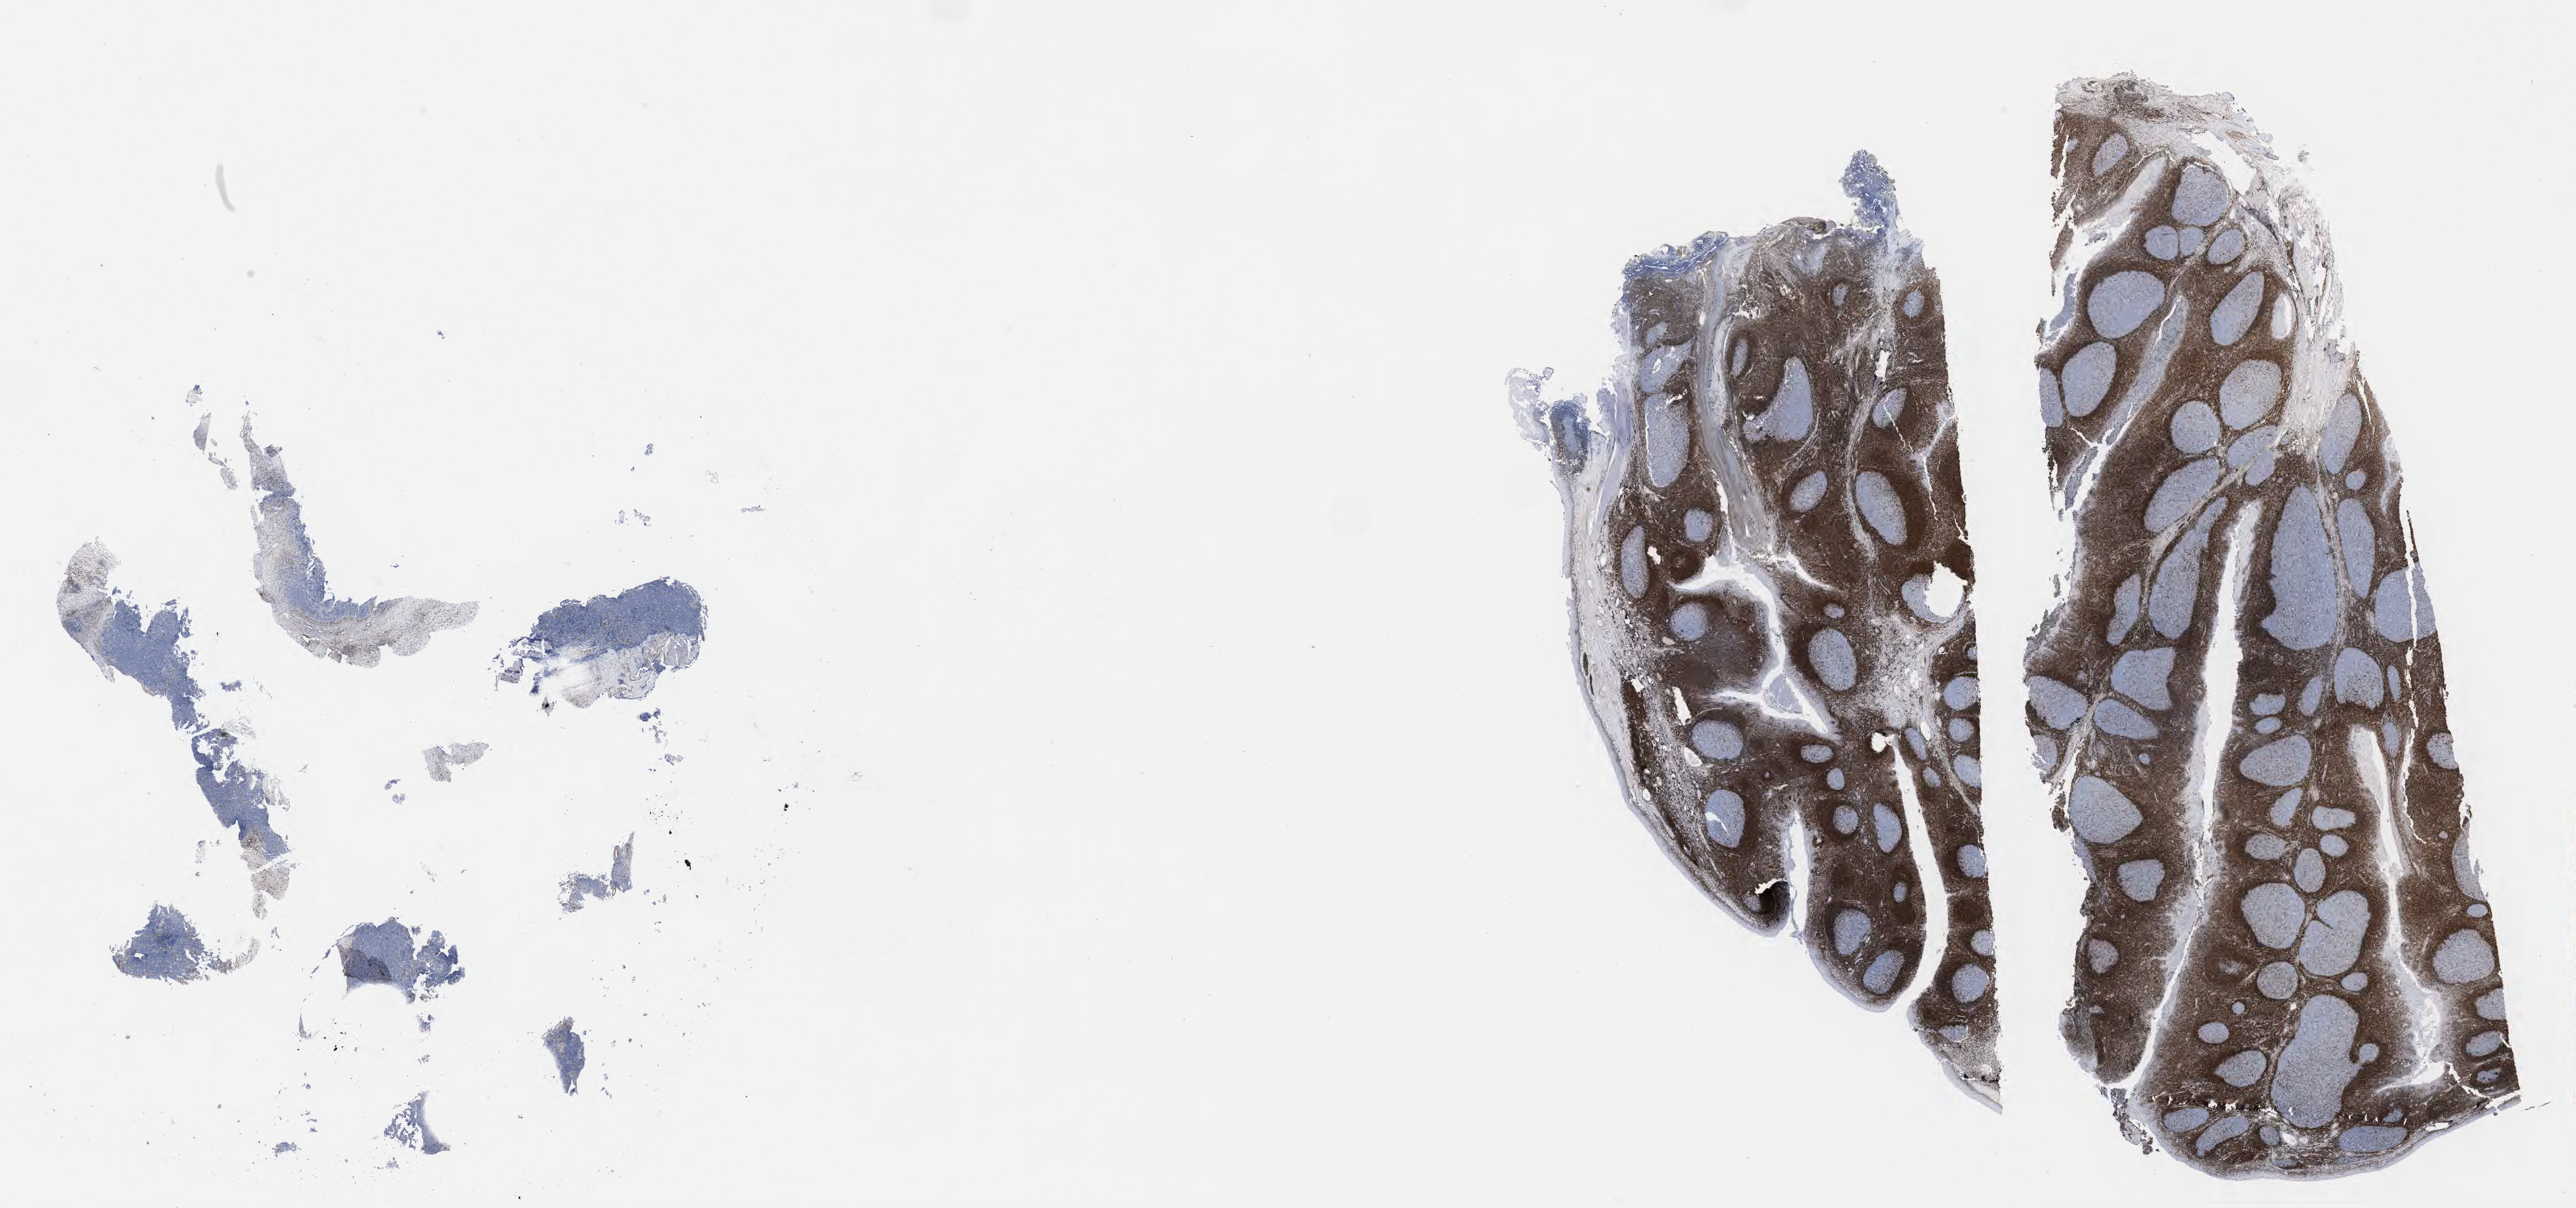
IHC for BCL2, whole-slide image — a low-resolution overview of the entire scanned area, about 31.7 x 14.9 mm. Tumor tissue. Female patient; age at initial diagnosis 9 years.
Histologic diagnosis: Burkitt lymphoma, NOS.